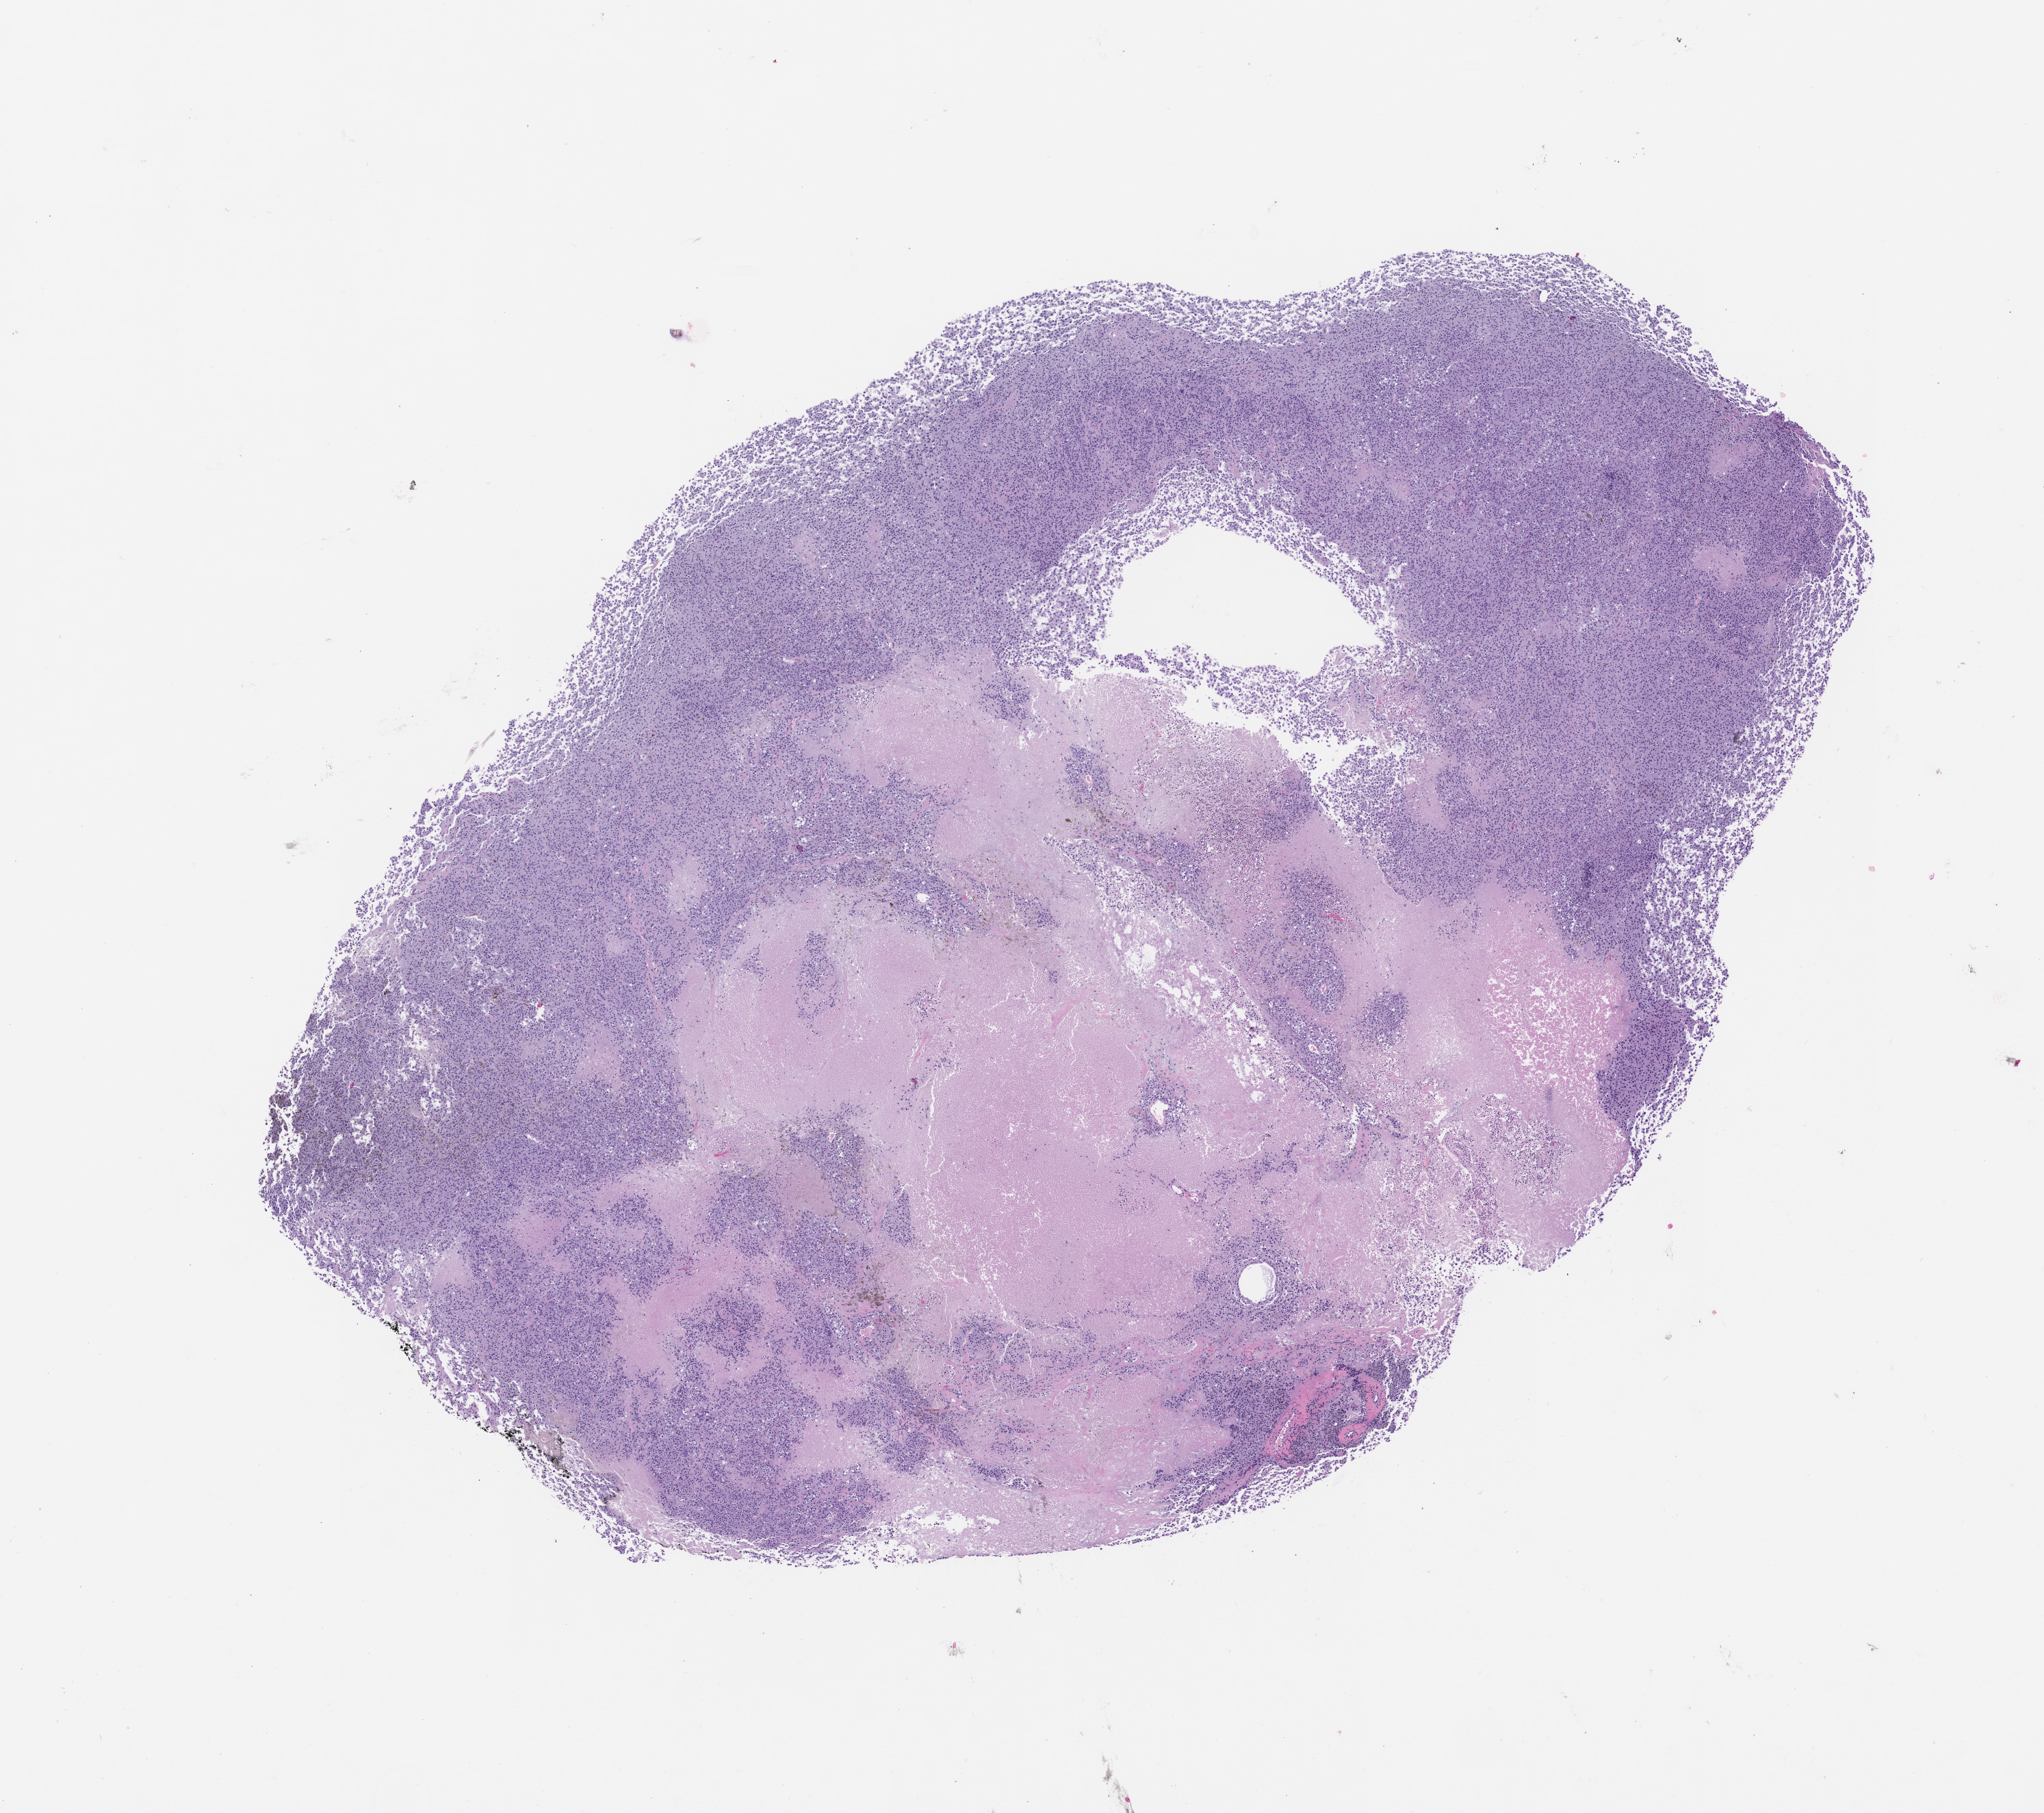
Whole-slide image, hematoxylin and eosin (H&E): patient-derived xenograft (human tumor grown in a mouse), passage 0, a low-resolution overview of the entire scanned area, about 12.0 x 10.6 mm; formalin-fixed paraffin-embedded section; tumor site category: skin.
Originating patient diagnosis: Melanoma.